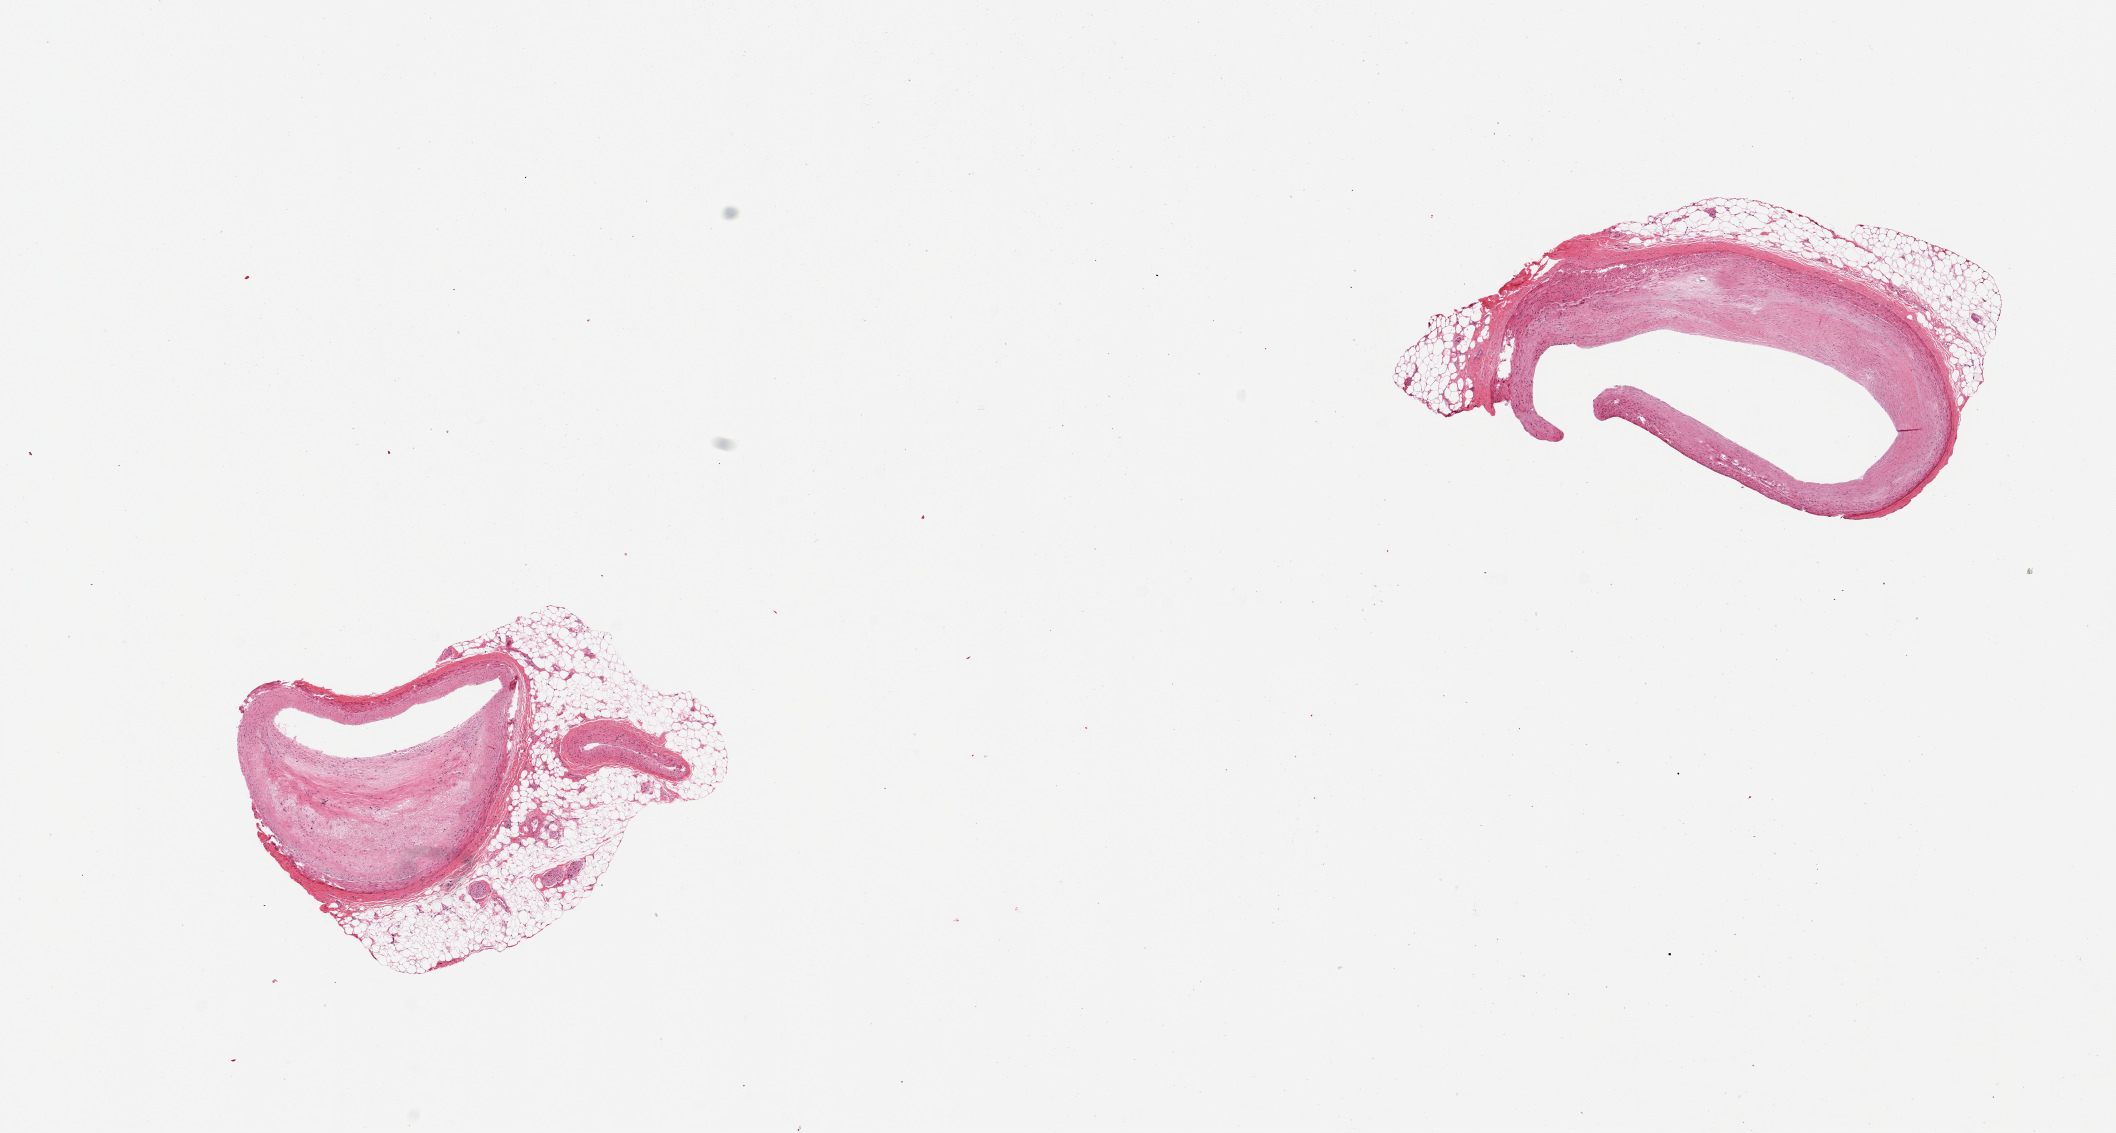
Haematoxylin and eosin whole-slide image — whole scanned area (about 16.7 x 9.0 mm) shown as a low-resolution overview; PAXgene-fixed, paraffin-embedded tissue; section of coronary artery (target tissue); tissue donor sample. Male donor.
Pathologist's review note for this sample: 2 pieces; both with atherosclerotic plaque and attached adipose tissue. Smaller piece has ~50-75% luminal occlusion.